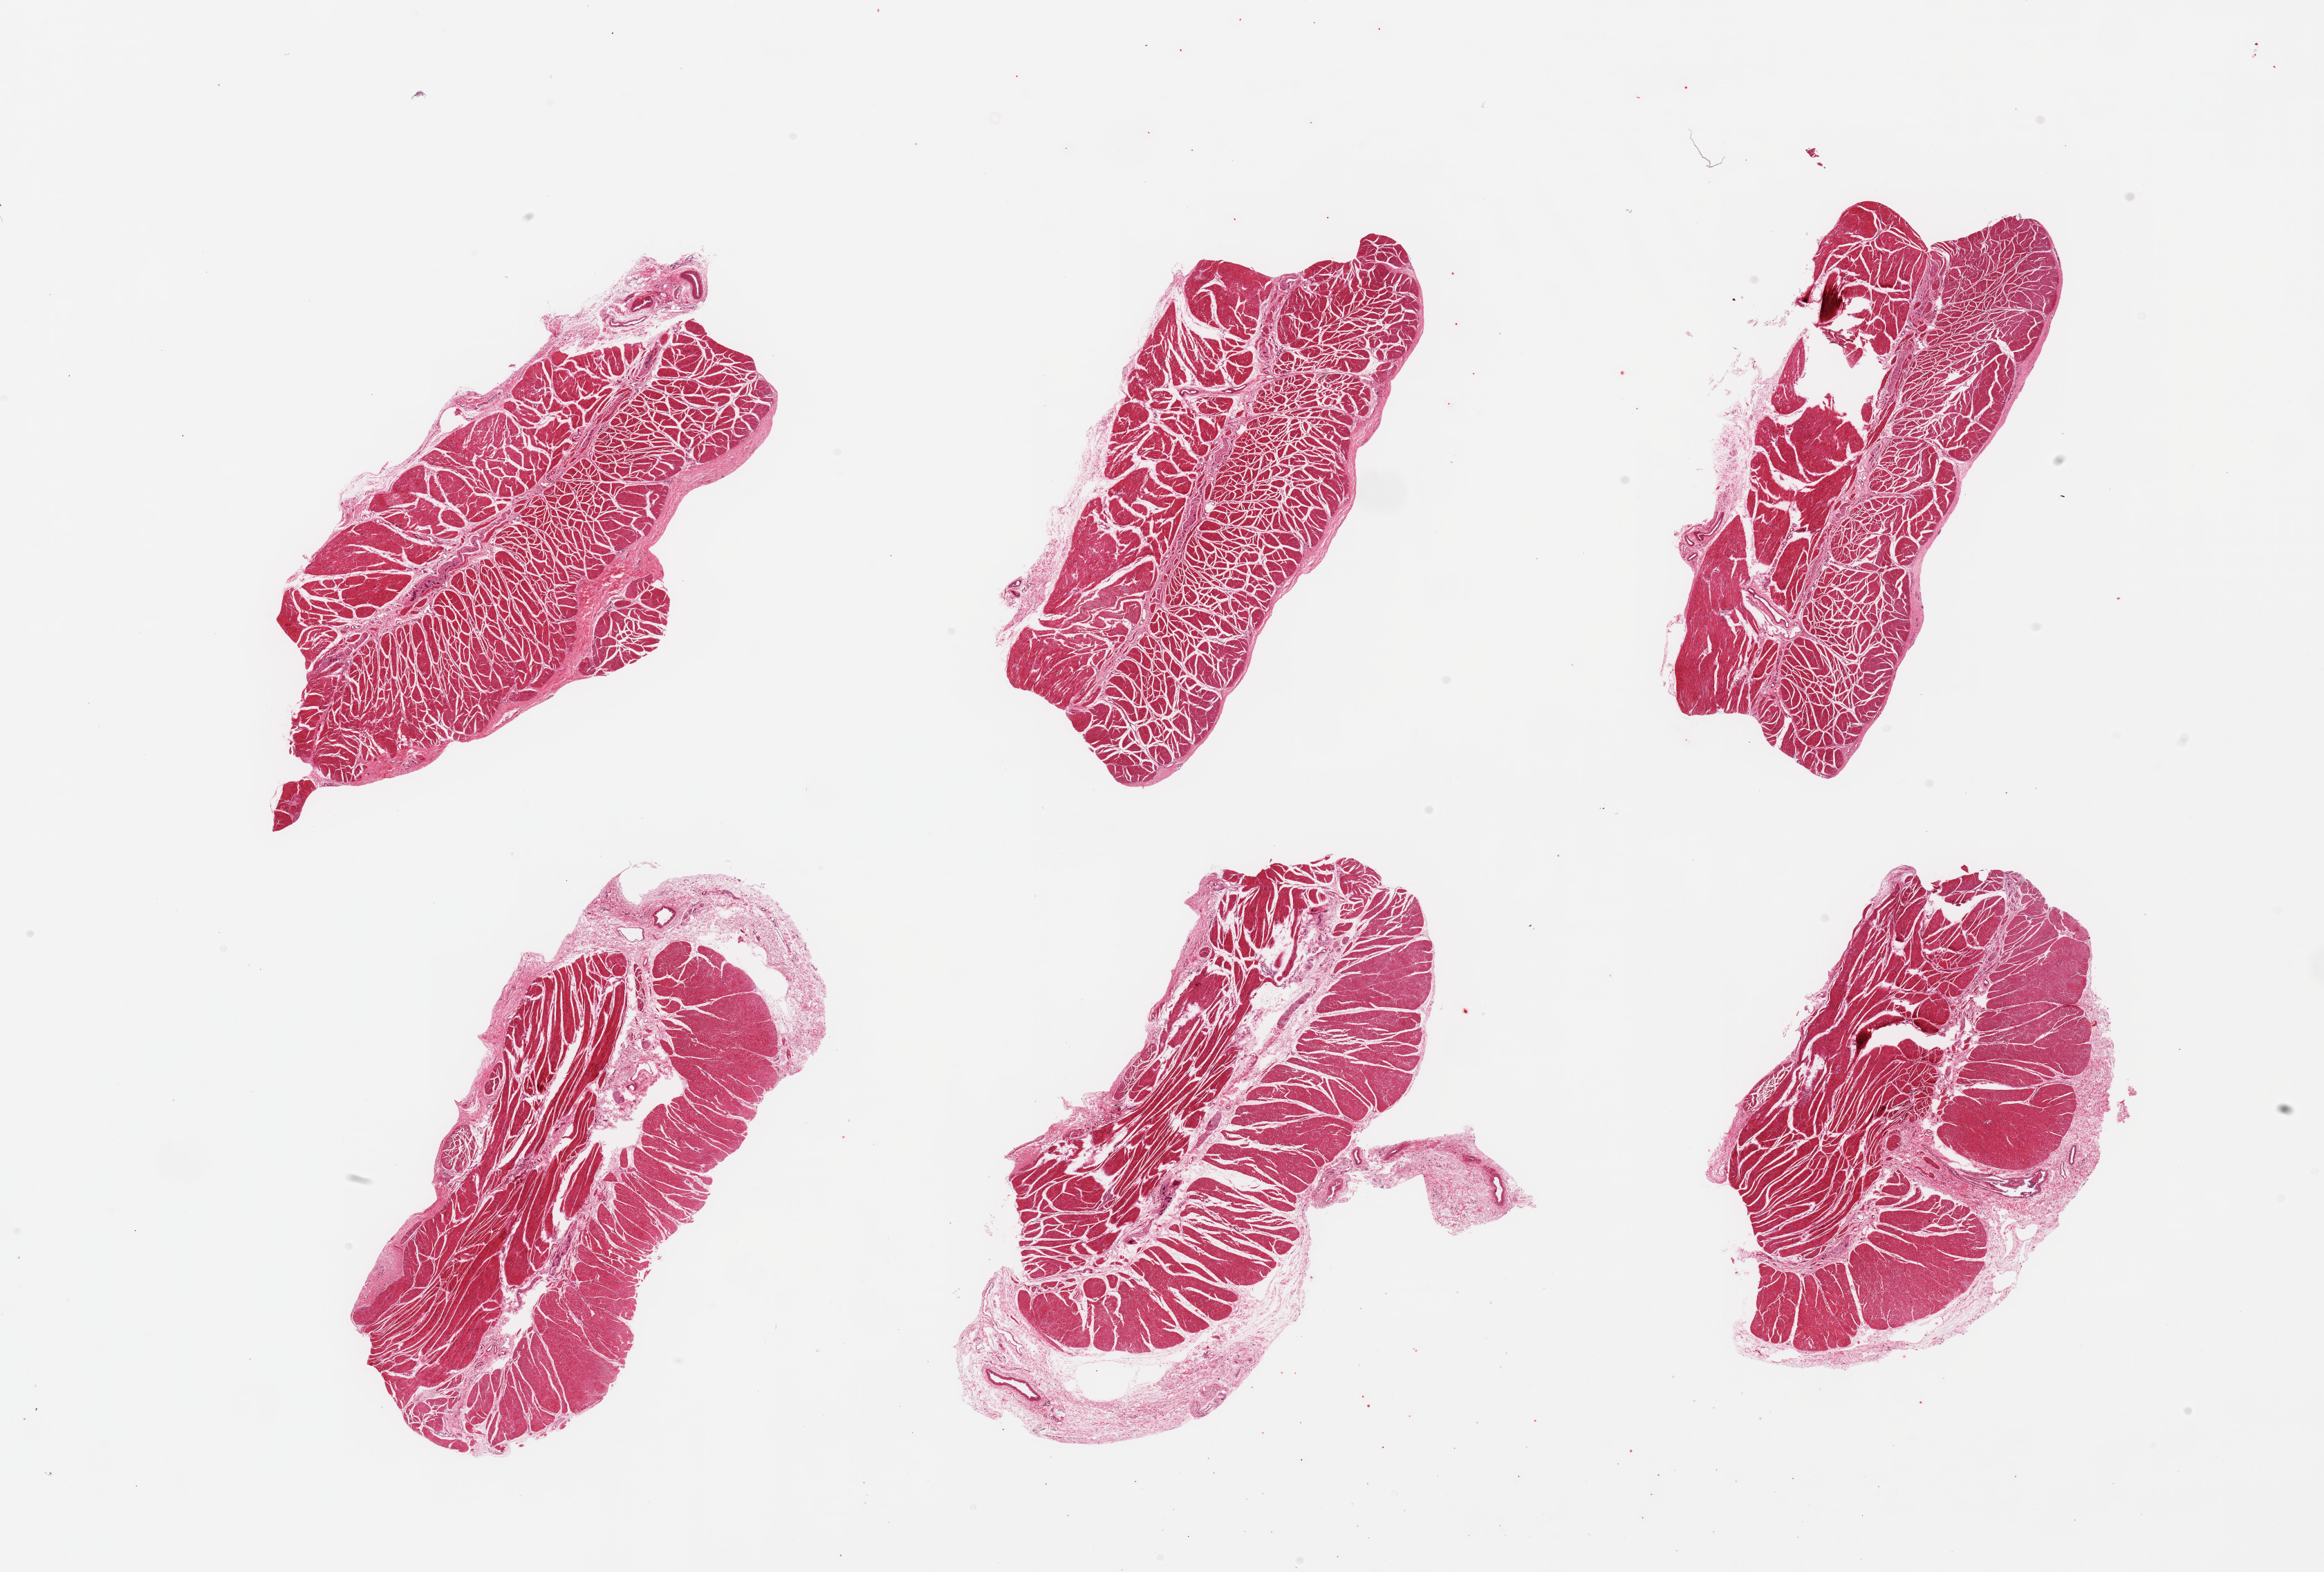
Haematoxylin and eosin whole-slide image, brightfield, whole scanned area (about 26.6 x 18.0 mm) shown as a low-resolution overview; PAXgene-fixed paraffin-embedded (PFPE) section; section of esophageal muscle (target tissue); tissue donor sample.
Pathologist's review note for this sample: 6 pieces; well dissected muscle, small amount of adjacent stroma.